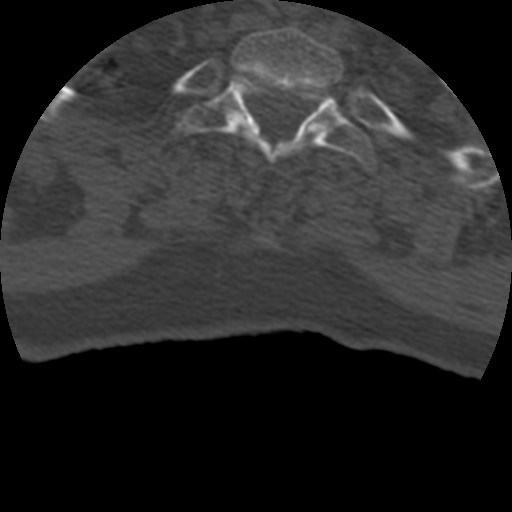
CT including the spine, one axial slice. Slice 373 of 399 in the series (ordered by position). Reconstruction kernel STANDARD. 120 kVp. Bone window (W 1800 / L 400 HU). 1.25 mm slice thickness. 512 × 512 image matrix, field of view 160 × 160 mm. Patient age 69 years. Case-level facts recorded for this patient, not image findings: primary cancer: prostate.
Structures marked on this image (semi-automatic segmentation, software-assisted and operator-edited):
- T1 vertebra: bounding box <233,27,343,126> (left, top, right, bottom; pixels)
- T2 vertebra: <171,74,378,170>